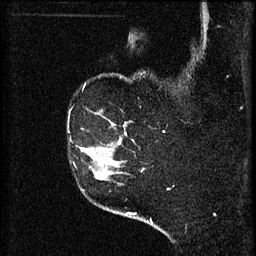
Breast MRI (dynamic contrast-enhanced), one sagittal slice. Slice 48 of 60 in the series (ordered by position). 3 images stored at this slice position (order not interpretable as contrast timing). 1.5 T. TE 4.2 ms, TR 8.2 ms. 2 mm slice thickness. 256 × 256 image matrix. Patient: female, 49 years.
Outlined on this slice (semi-automatically segmented with operator editing):
- analysis volume of interest (the breast-tissue region the enhancement analysis was run in; not a lesion): bounding box (x1, y1, x2, y2) in pixels: (78, 146, 105, 177)
- tumour enhancement mask (voxels above the 70 % enhancement threshold inside the analysis volume of interest): (81, 148, 105, 177)